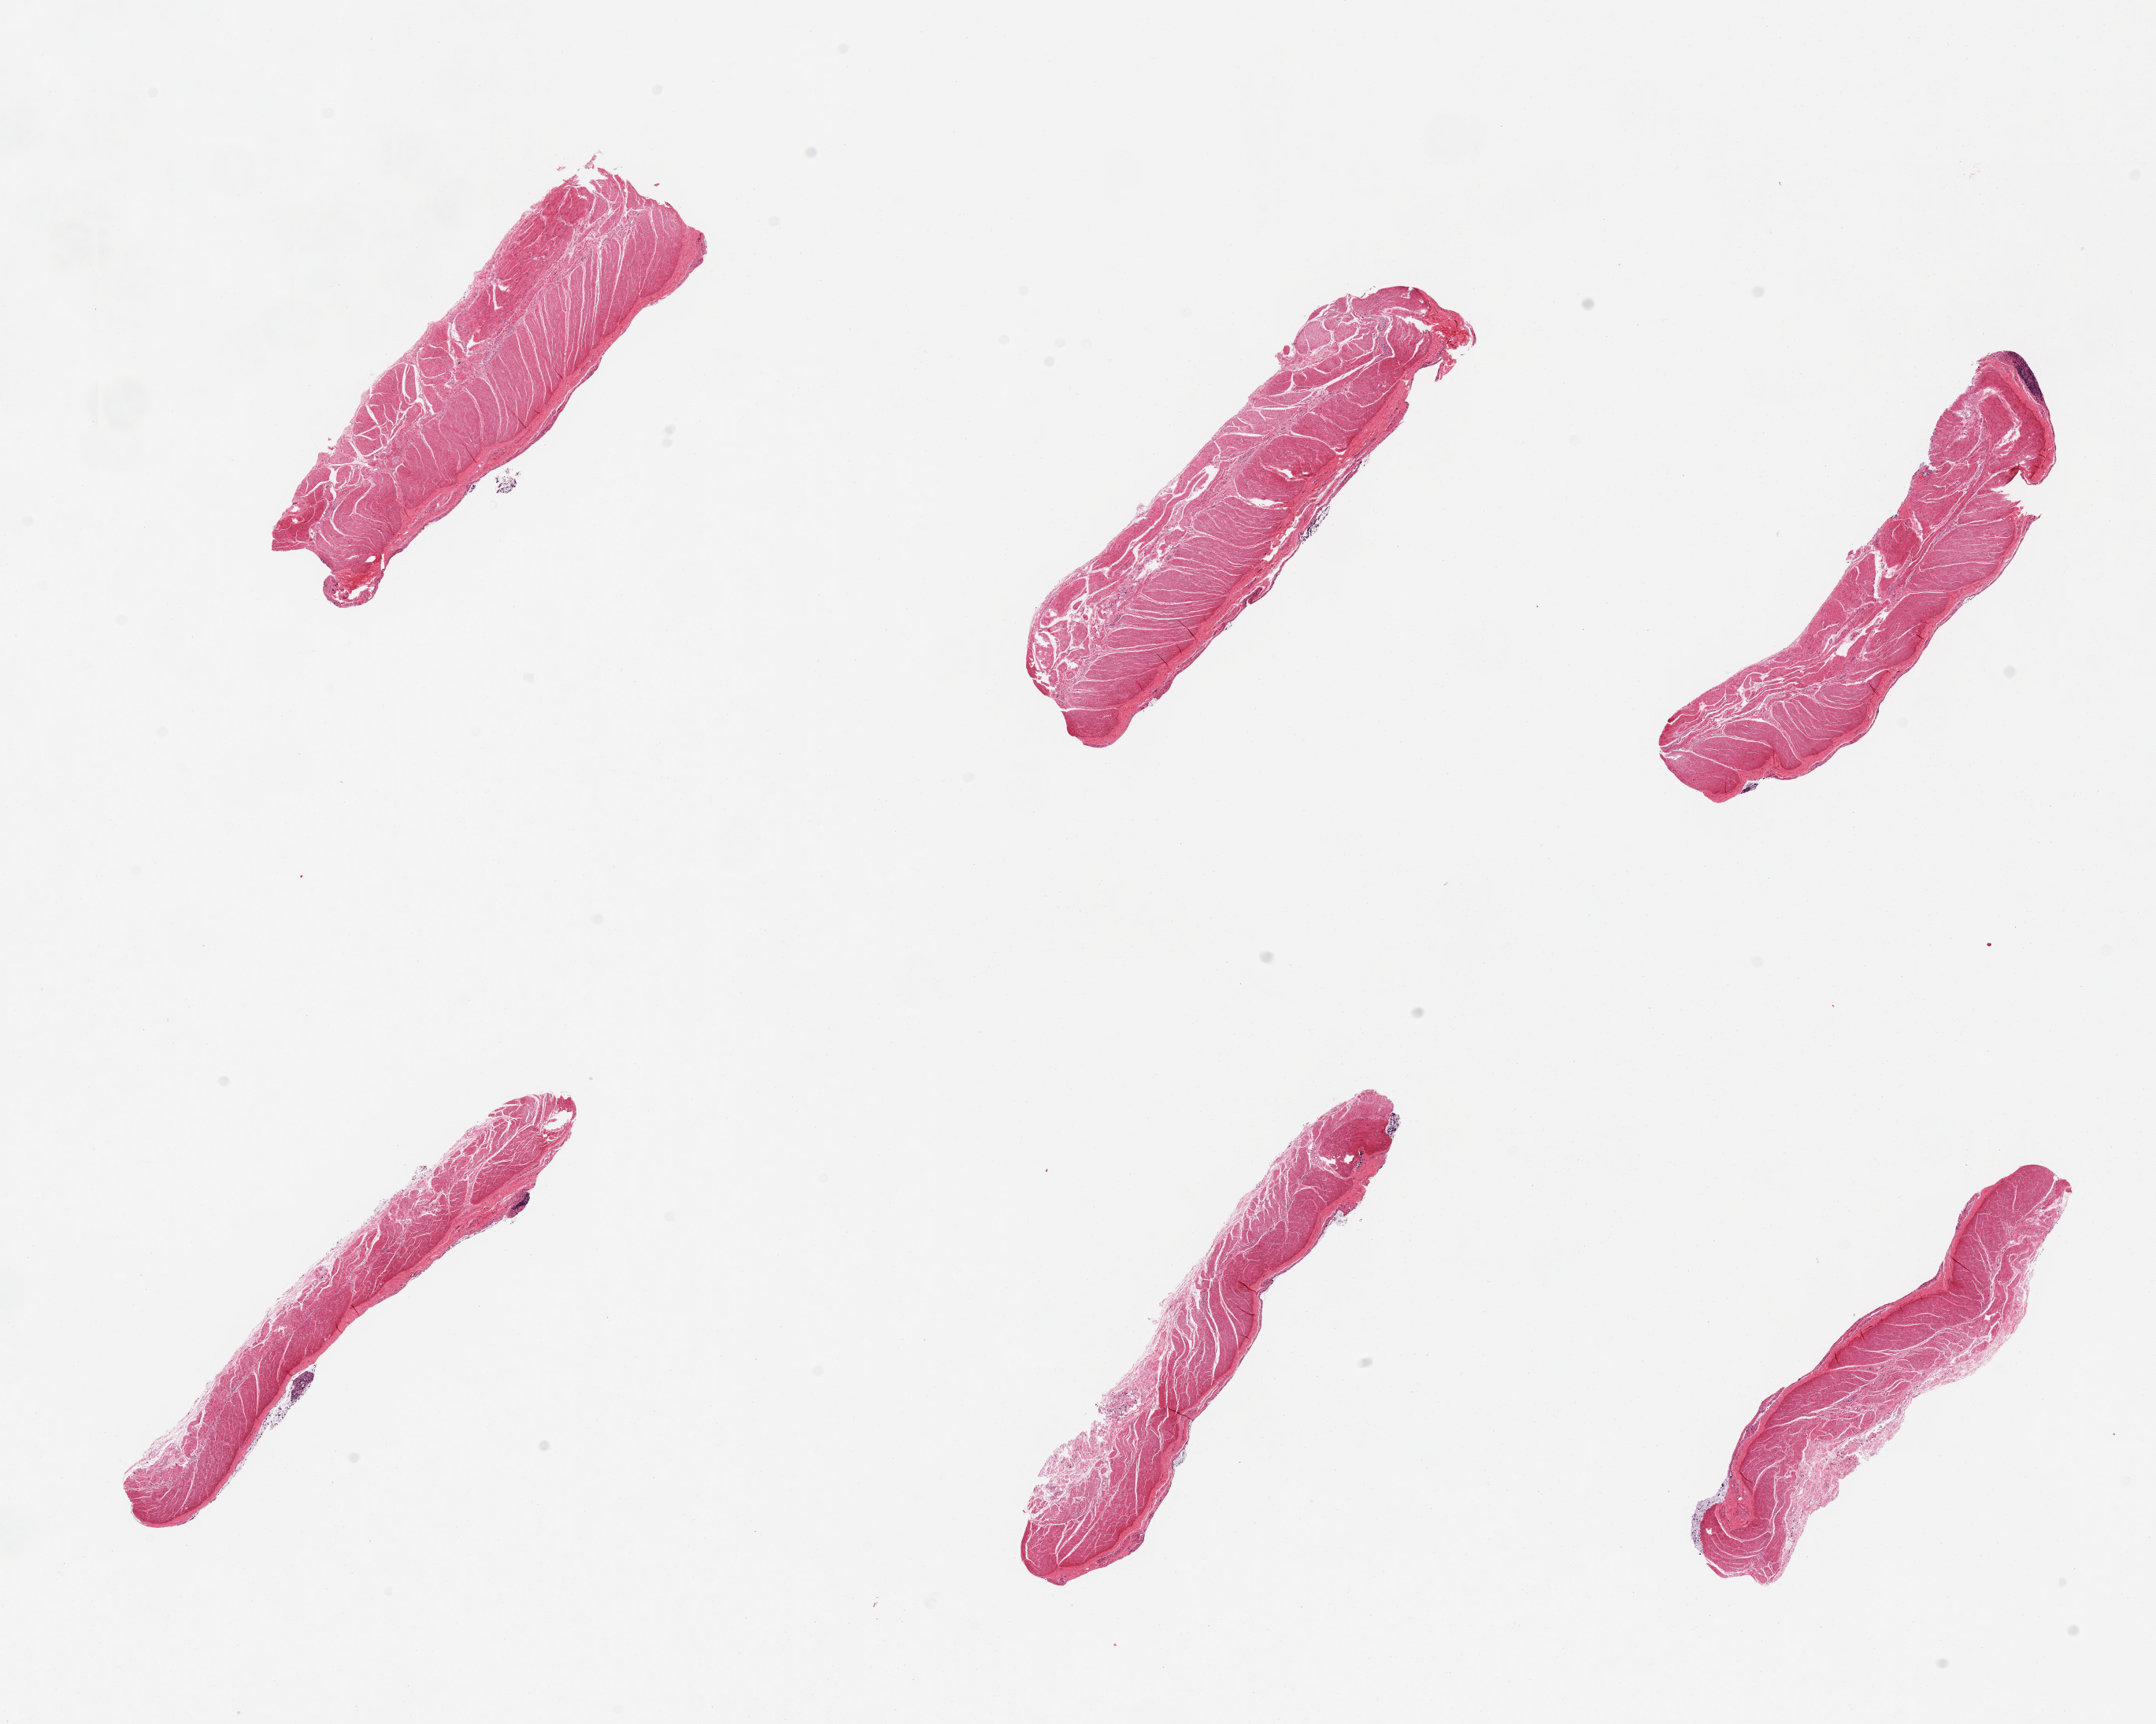
Digitized H&E-stained section, whole scanned area (about 21.7 x 17.3 mm, acquisition: 20x scan) shown as a low-resolution overview, PAXgene-fixed paraffin-embedded (PFPE) section, target tissue: sigmoid colon, tissue donor sample.
Reviewer comment on this tissue sample: 6 pieces, muscularis; good specimens4.